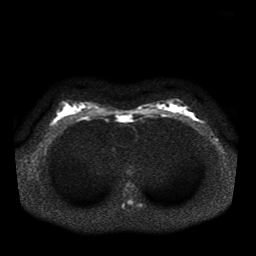
Breast MRI, one axial slice. Position 22 of 41 along the scan axis. Diffusion-weighted series; image 2 of 4 stored at this slice position (different b-values; order by instance number). 1.5 T. 5 mm slice thickness. 256 × 256 image matrix, field of view 330 × 330 mm. Female patient.
Structures marked on this image (manually delineated by an expert):
- tumour on diffusion-weighted imaging: bounding box <188,113,193,116> (left, top, right, bottom; pixels)